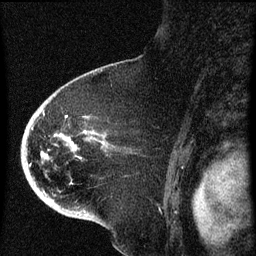
Breast MRI (dynamic contrast-enhanced), one sagittal slice. Position 46 of 60 along the scan axis. Dynamic contrast-enhanced series, image 2 of 4 at this slice position (ordered by acquisition). 1.5 T. TE 4.2 ms, TR 8 ms. 2 mm slice thickness. 256 × 256 image matrix, field of view 180 × 180 mm. Female patient, age 71 years.
Structures marked on this image (semi-automatically segmented with operator editing):
- analysis volume of interest (the breast-tissue region the enhancement analysis was run in; not a lesion): bounding box (x1, y1, x2, y2) in pixels: (32, 86, 124, 205)
- tumour enhancement mask (voxels above the 70 % enhancement threshold inside the analysis volume of interest): (43, 112, 107, 159)